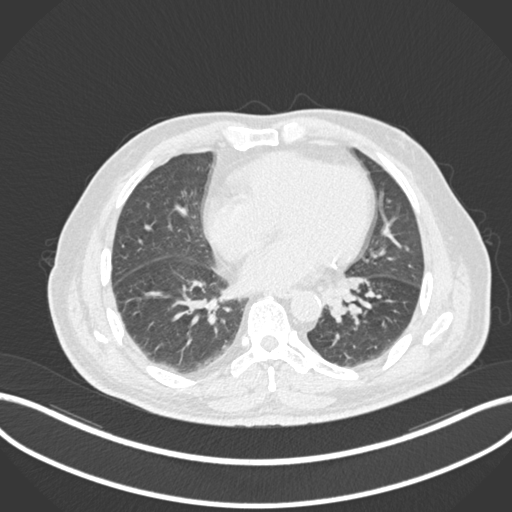
Chest CT, one axial slice; position 43 of 161 along the scan axis; 120 kVp; lung window (W 1500 / L -600 HU); 512 × 512 image matrix, field of view 400 × 400 mm. Male patient, age 71 years. From the clinical record (not read from this slice): clinical TNM (as recorded): T1b N0 M0.
Annotated regions visible in this slice (bounding box drawn by a radiologist):
- lung tumour (recorded histology: squamous cell carcinoma): bounding box (x1, y1, x2, y2) in pixels: (328, 276, 372, 324)